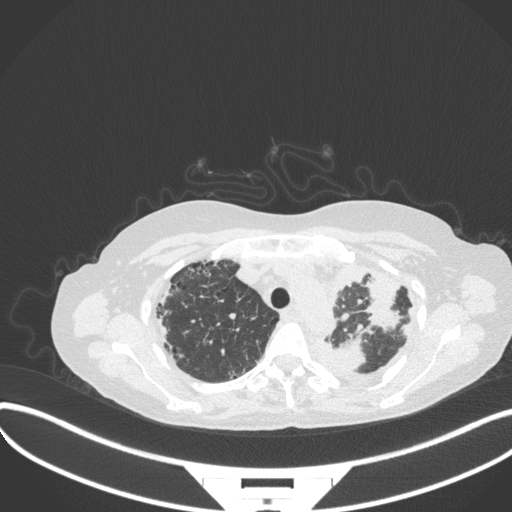
Chest CT, one axial slice; slice 270 of 373 in the series (ordered by position); reconstruction kernel B31f; lung window (W 1500 / L -600 HU); 512 × 512 image matrix. Female patient, age 56 years. From the clinical record (not read from this slice): clinical TNM (as recorded): T1 N0 M0.
Outlined on this slice (bounding box drawn by a radiologist):
- lung tumour (recorded histology: adenocarcinoma): box from (x=329, y=333) to (x=364, y=373) px
- lung tumour (recorded histology: adenocarcinoma): (x=361, y=272)–(x=403, y=333)